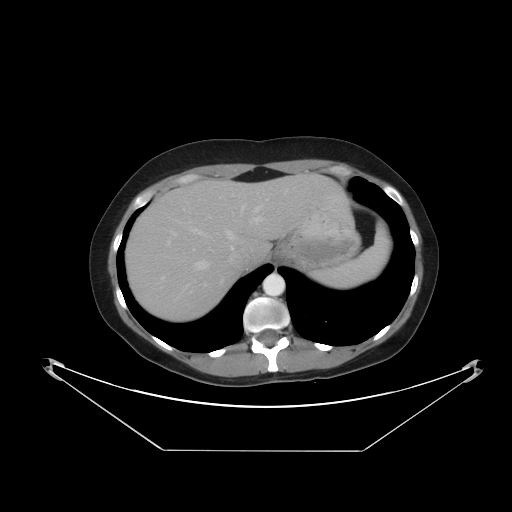
Contrast-enhanced abdominal CT, one axial slice. Position 37 of 48 along the scan axis. Reconstruction kernel STANDARD. Intravenous contrast given. Soft-tissue window (W 400 / L 40 HU). 5 mm slice thickness. 512 × 512 image matrix, field of view 482 × 482 mm. Female patient, age 38 years. Case-level facts recorded for this patient, not image findings: diagnosis: colorectal cancer liver metastases, imaged before liver resection; multiple liver metastases: yes; largest metastasis: 2.5 cm; disease in both lobes: no.
Annotated regions visible in this slice (outlined manually by an expert reader):
- hepatic veins: bounding box <193,203,264,269> (left, top, right, bottom; pixels)
- liver: <127,176,349,323>
- planned liver remnant (the part of the liver to remain after resection): <197,176,349,260>
- portal vein (with intrahepatic branches): <173,218,260,235>